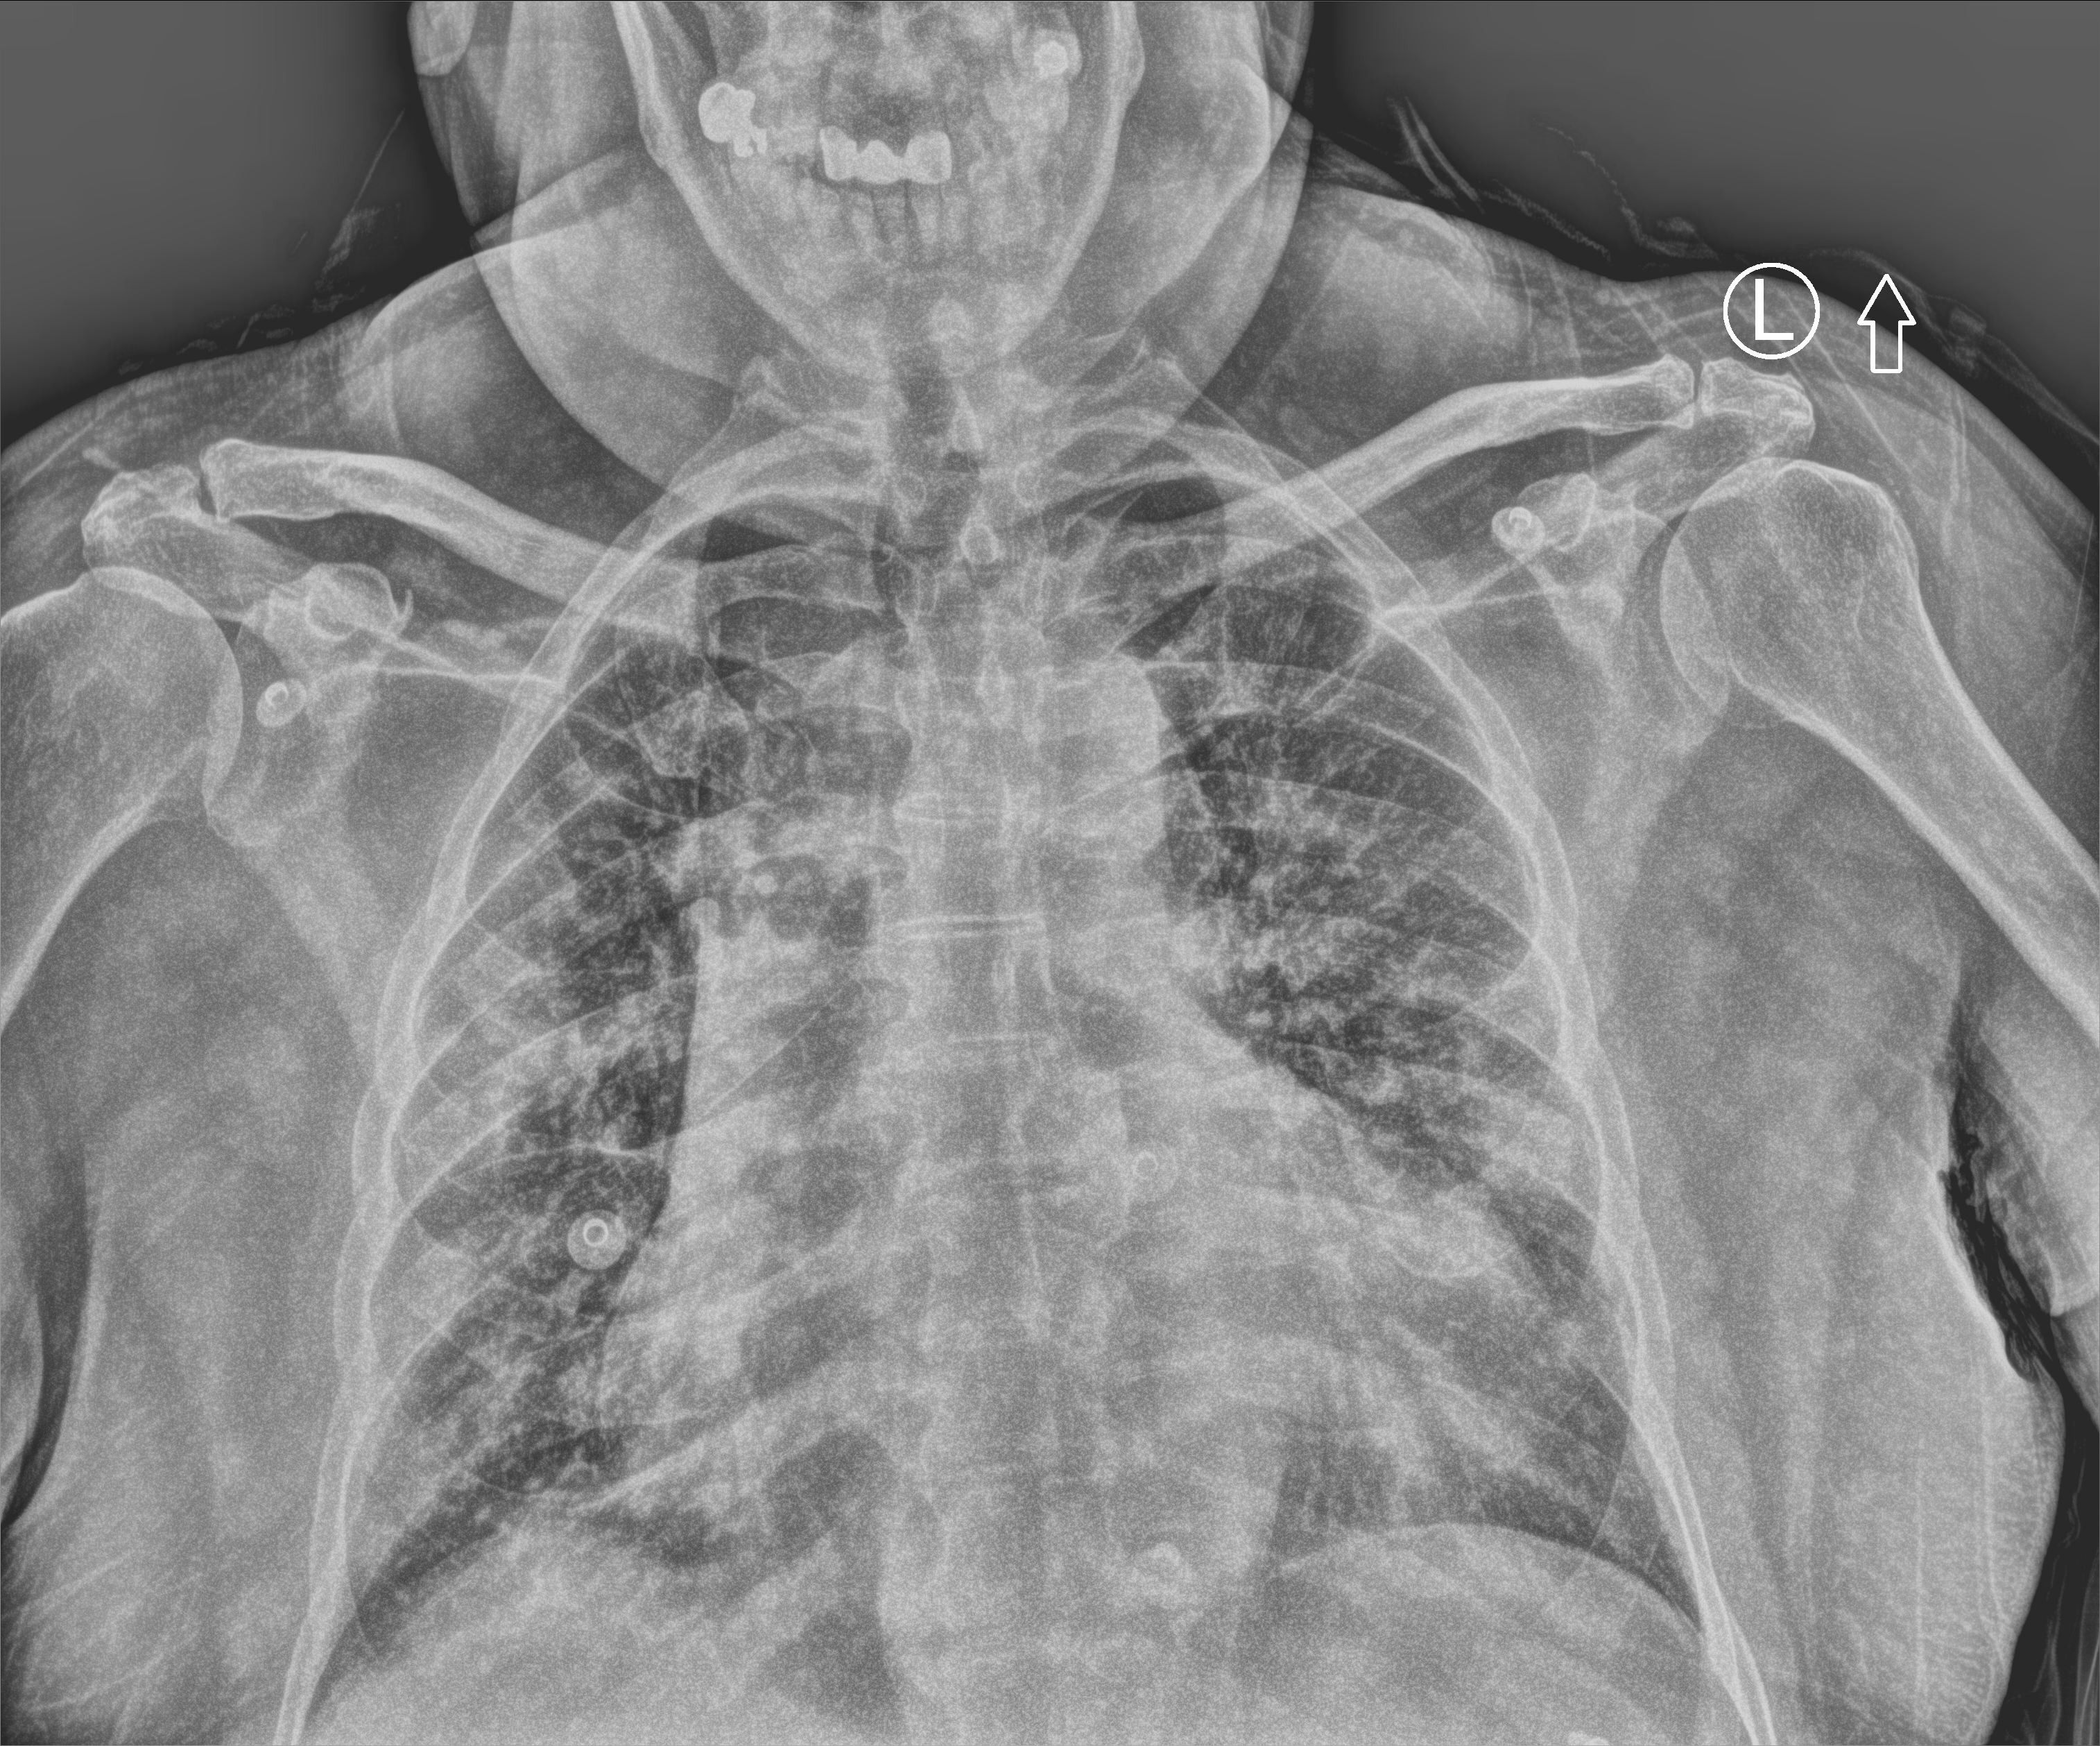
Portable chest radiograph. Male patient hospitalised with COVID-19, age 60–74 years.
Admission-level facts for this patient (not findings on this image; timing relative to this image not recorded): mechanically ventilated during this hospital stay: yes; admitted to intensive care during this hospital stay: yes; smoking status (admission record): never.